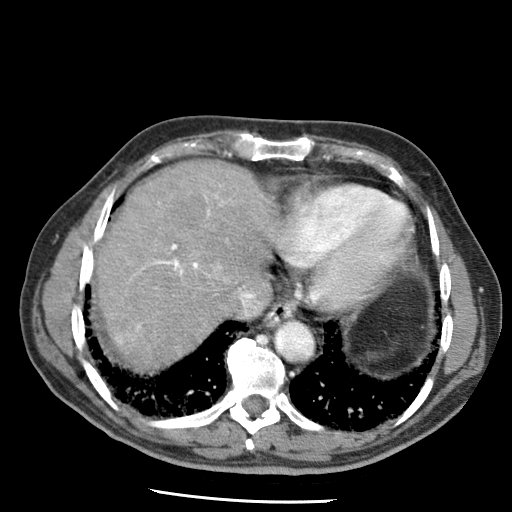
Contrast-enhanced abdominal CT (liver protocol), one axial slice. Position 57 of 79 along the scan axis. Reconstruction kernel STANDARD. 120 kVp. Soft-tissue window (W 400 / L 40 HU). 512 × 512 image matrix, field of view 320 × 320 mm. From the clinical record (not read from this slice): diagnosis: hepatocellular carcinoma (patient treated with transarterial chemoembolisation; whether this scan precedes or follows treatment is not stated here); TNM stage (as recorded): Stage-IIIA; Child-Pugh class: A; tumour differentiation: moderately differentiated; tumour nodularity: multinodular.
Annotated regions visible in this slice (semi-automatic segmentation, software-assisted and operator-edited):
- abdominal aorta: box from (x=276, y=324) to (x=313, y=361) px
- liver parenchyma outside the tumour (the mass and vessels are separate outlines, so this box may not span the whole liver): (x=96, y=160)–(x=274, y=368)
- liver vessels: (x=116, y=195)–(x=224, y=343)